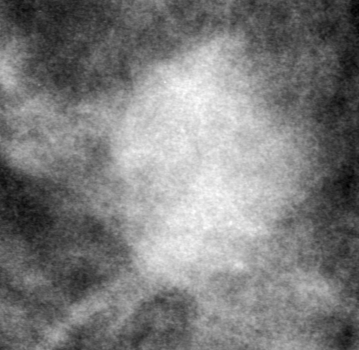
Cropped region of a digitized screen-film mammogram centred on a radiologist-marked abnormality, right breast, CC view.
- Mass, shape oval, margins obscured; BI-RADS assessment category 0 (incomplete: needs additional imaging); subtlety rating 5 on a 1 (subtle) to 5 (obvious) scale; pathology result (as recorded, not read from the image): benign.